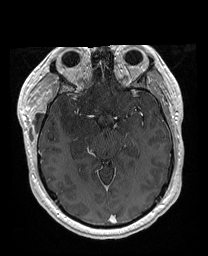
Brain MRI from a brain-tumour surgery series, one axial slice. Slice 108 of 176 in the series (ordered by position). T1-weighted post-contrast. 1 mm slice thickness. 208 × 256 image matrix. From the clinical record (not read from this slice): histopathology: Astrocytoma; WHO grade: 4; IDH mutation: yes; tumour location: Right Orbitofrontal Anterior Temporal Insular.
Outlined on this slice (outlined manually by an expert reader):
- previous resection cavity: box from (x=56, y=62) to (x=106, y=73) px